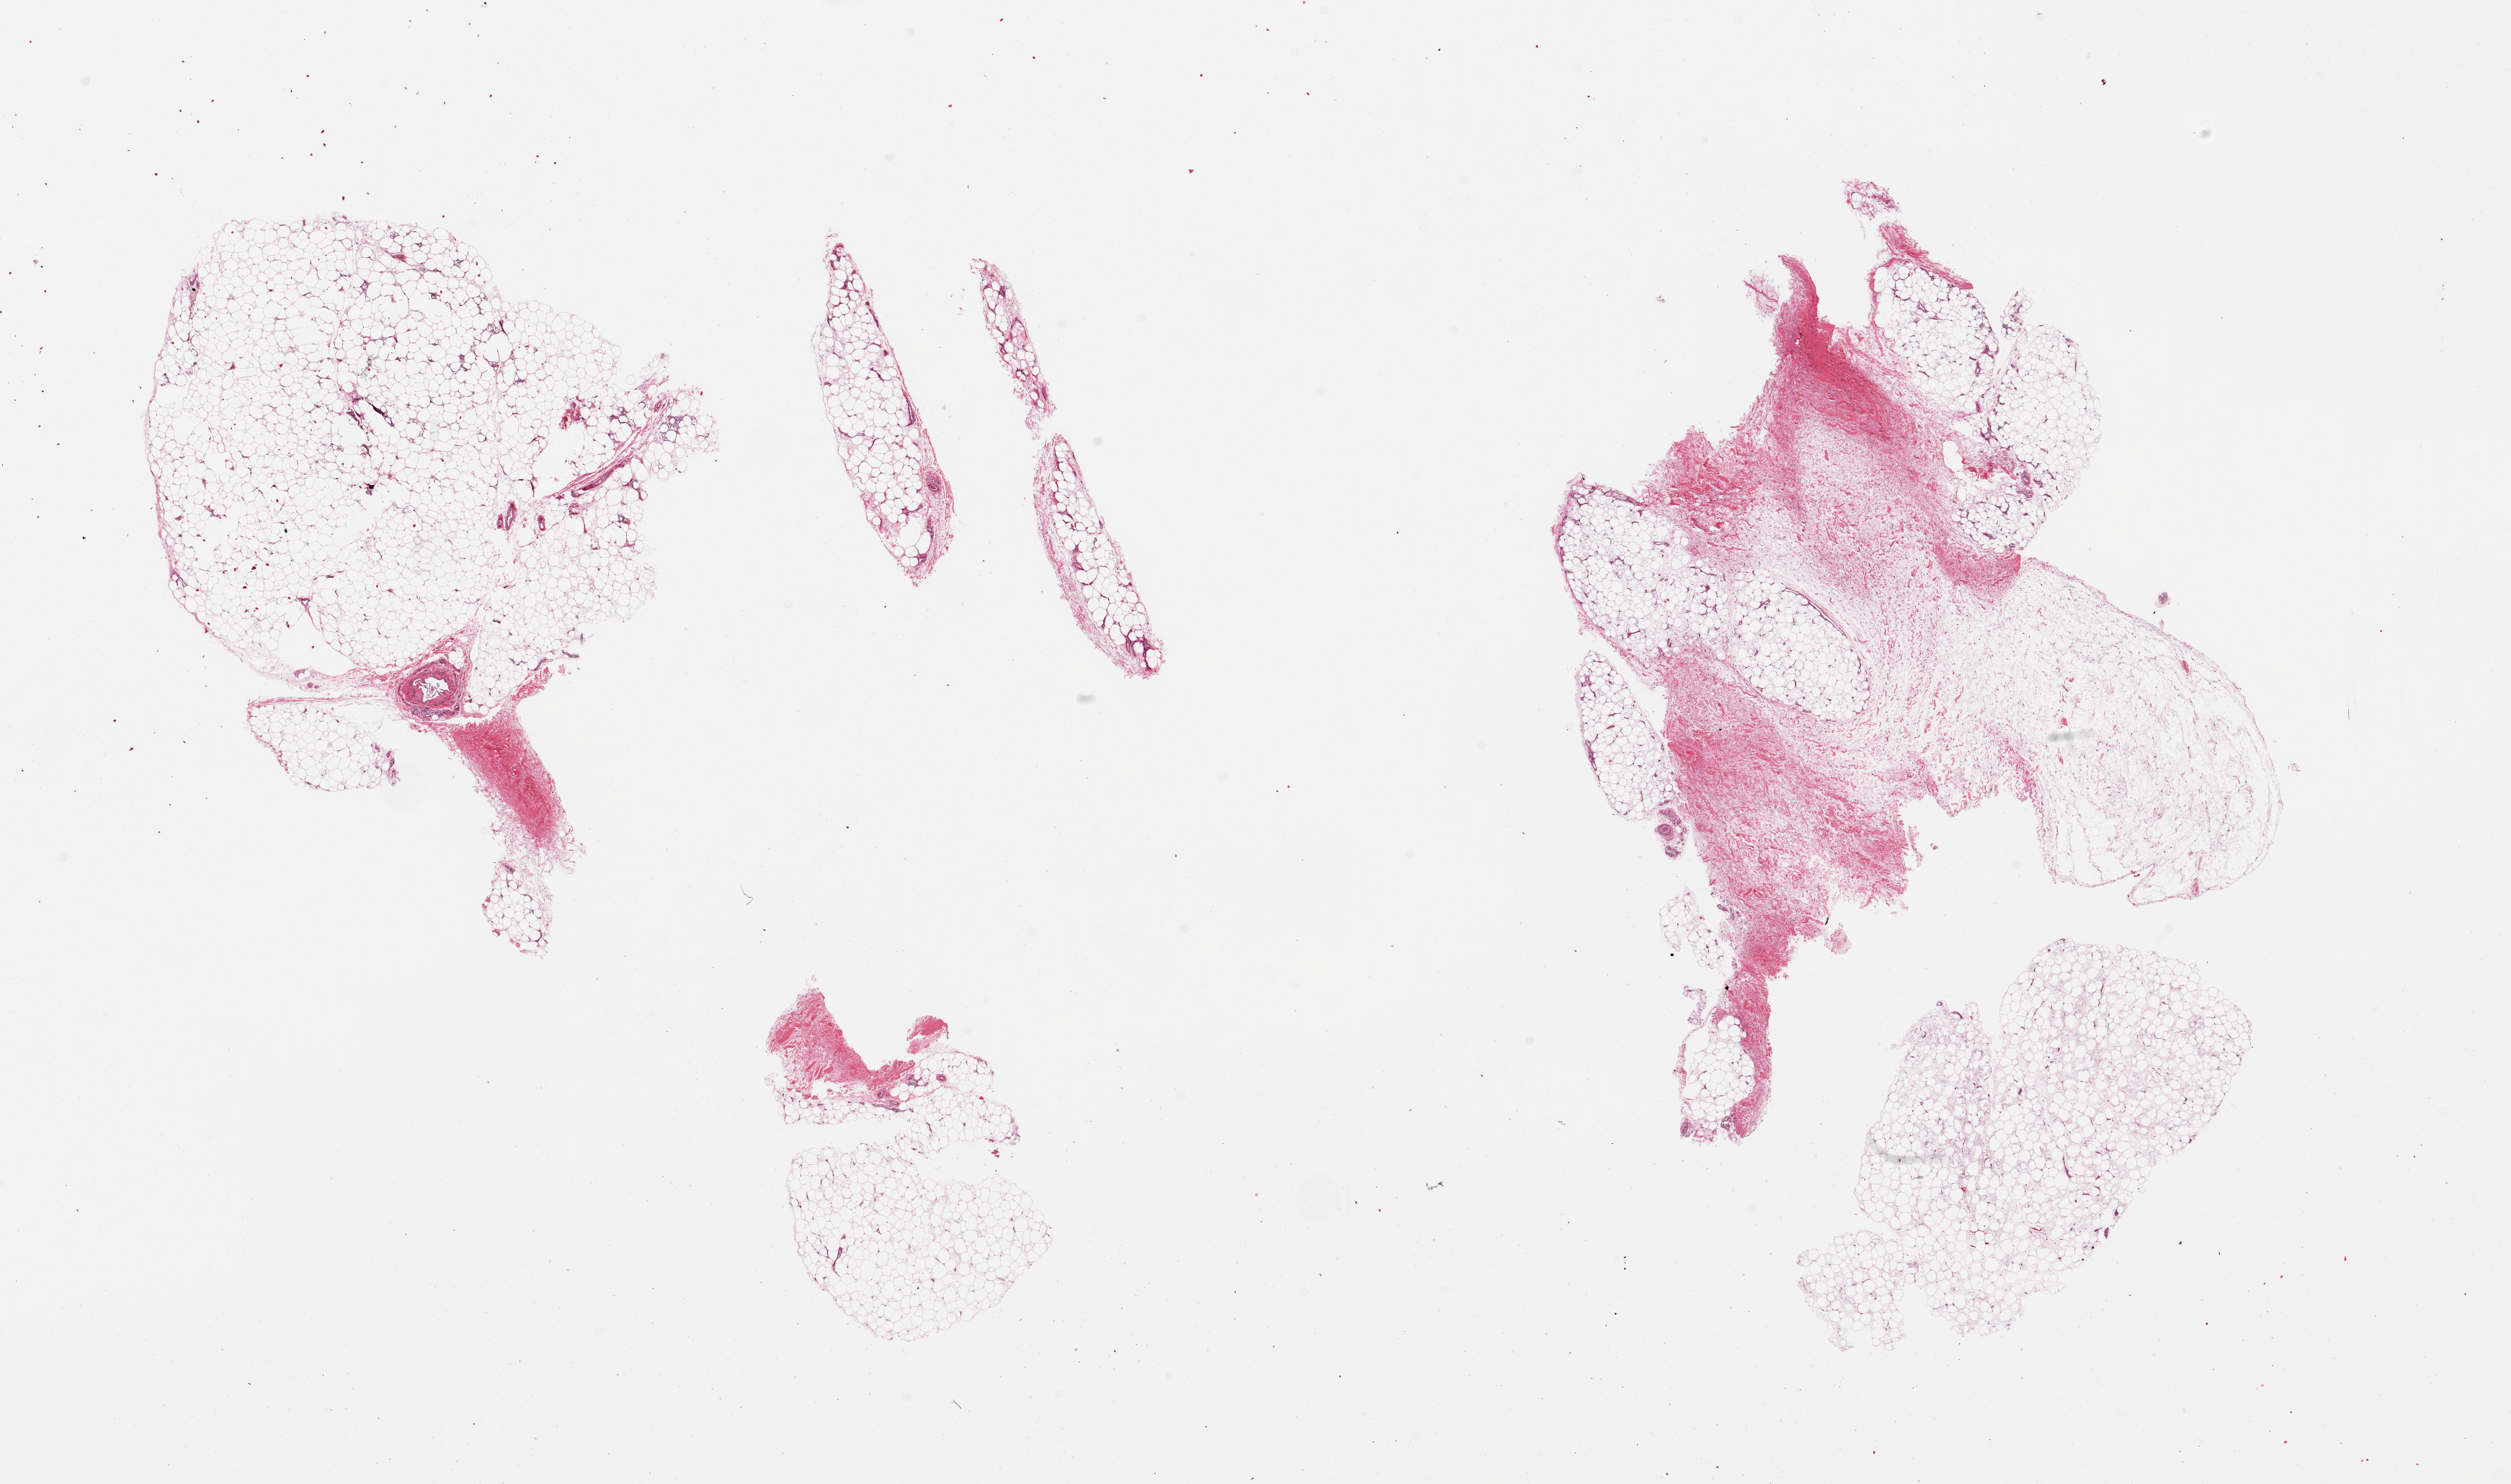
Hematoxylin and eosin (H&E) whole-slide image, brightfield, whole scanned area (about 27.6 x 16.3 mm) shown as a low-resolution overview, PAXgene-fixed, paraffin-embedded tissue, section of adipose tissue (target tissue), donor tissue sample. Male donor.
Review note (as recorded): 2 pieces; 1 piece has 20% fibrous content.